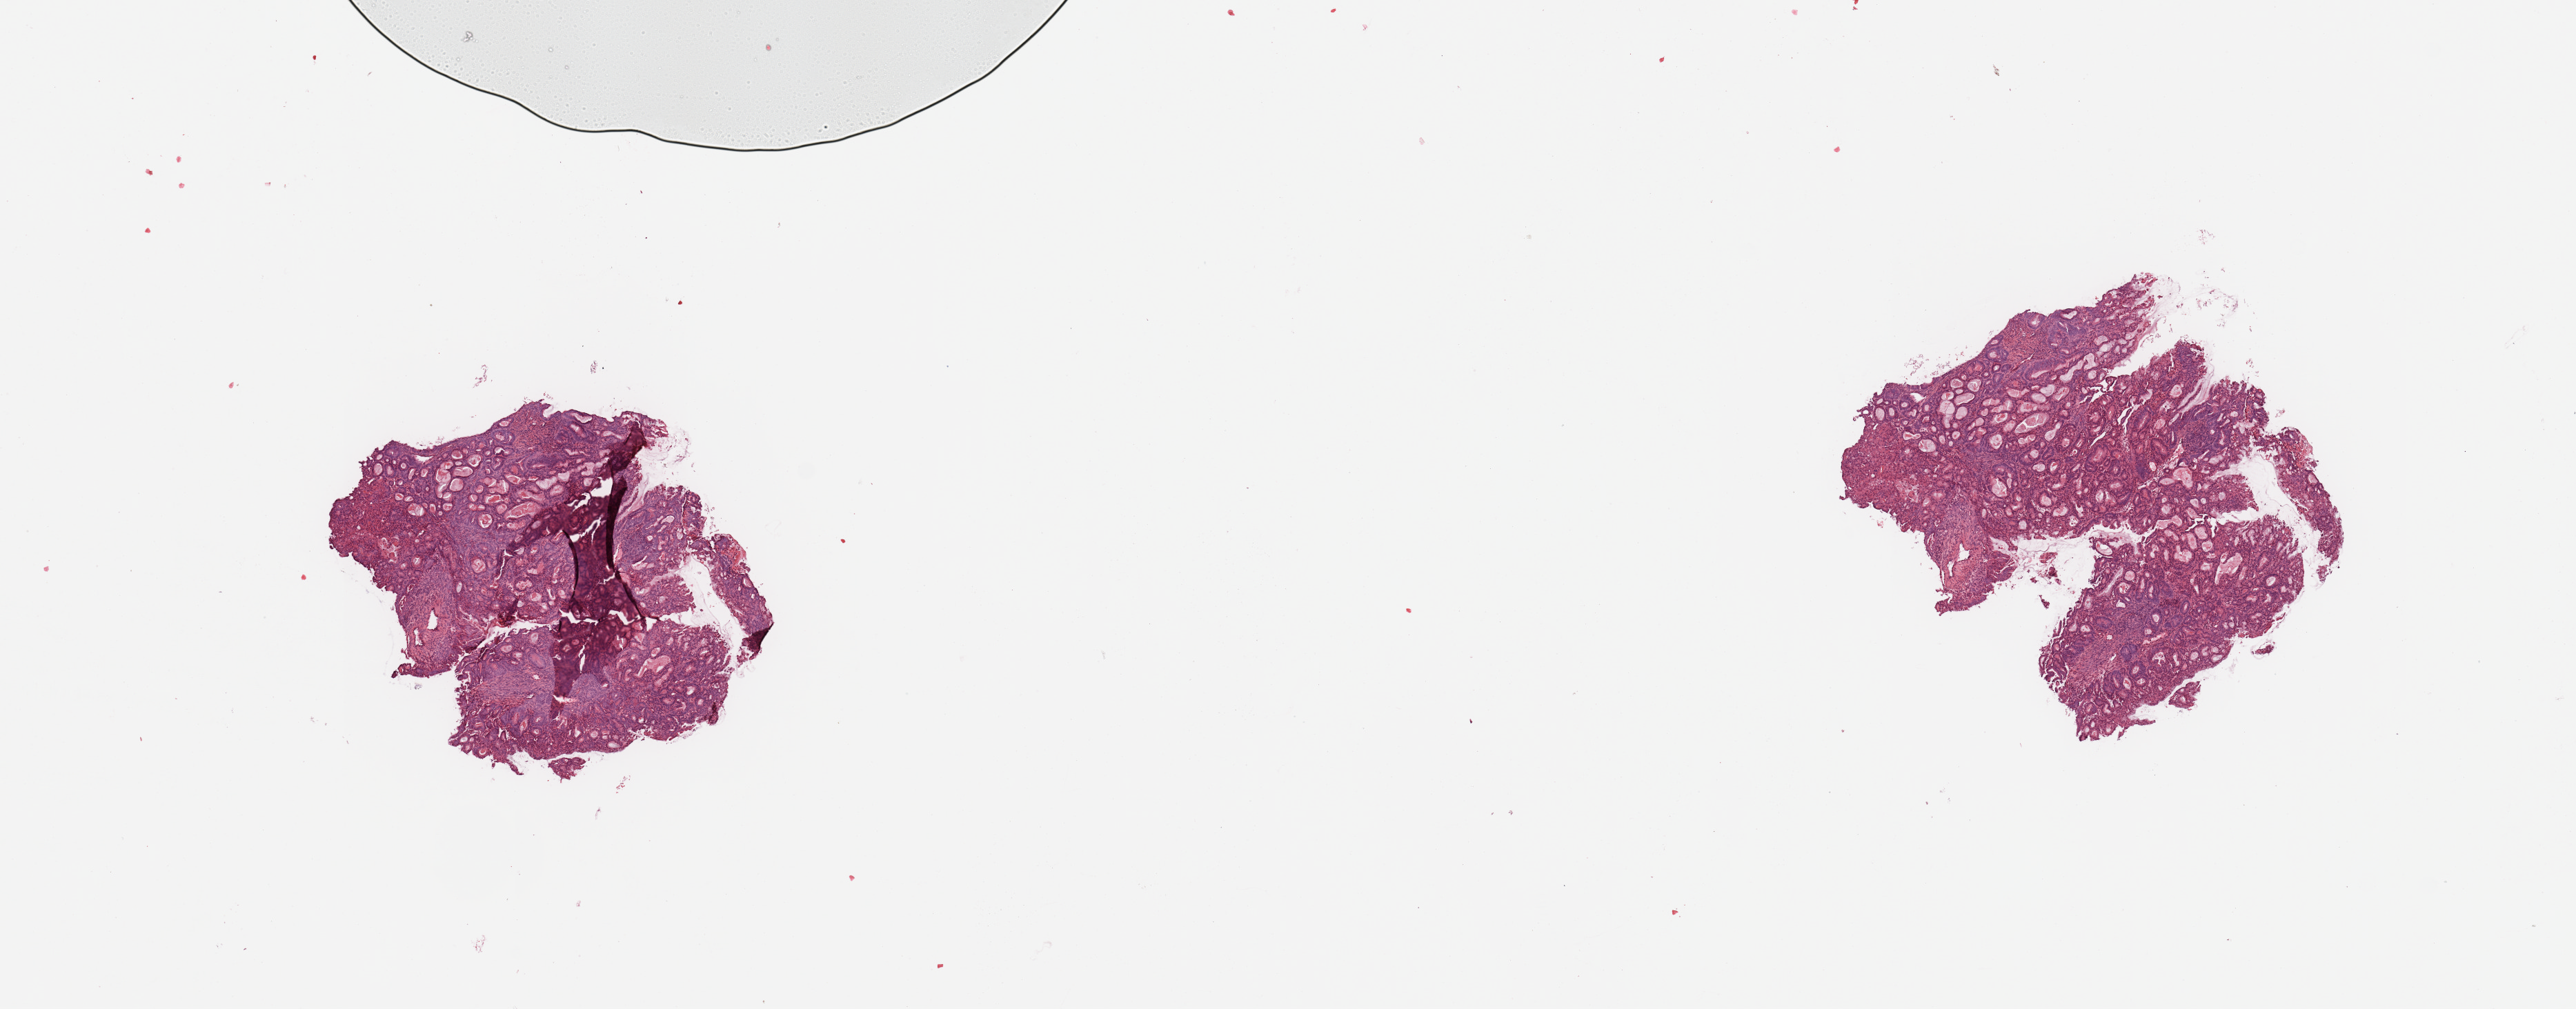
Digitized Hematoxylin and eosin (H&E) stained tissue section (whole slide), a low-resolution overview of the entire scanned area, about 14.8 x 5.8 mm (from a 20x scan), tumour tissue sample, sampled site: uterus. 77-year-old female patient. Histologic grade: G2 (moderately differentiated). Slide review estimates, as recorded: tumour nuclei 80%, necrosis 2%.
* histologic diagnosis: Endometrioid adenocarcinoma, NOS
* primary tumour site (as recorded): anterior endometrium
* AJCC pathologic stage: I